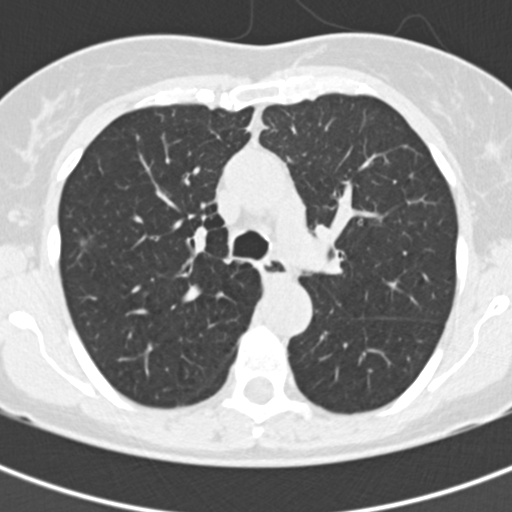
Chest CT (low-dose screening protocol), one axial image; baseline annual screen; lung window (W 1500 / L -600 HU); 2 mm slice thickness; slice 65 of 177 in the series. Female, age 60 years at enrolment. Current smoker at enrolment.
Expert-annotated lung lesion, box from (x=55, y=220) to (x=110, y=268) px. No non-calcified nodule or mass ≥4 mm was recorded by the screening reader at this exam. Official screen result: negative screen, no significant abnormalities. Lung cancer was diagnosed 861 days after this screen: bronchiolo-alveolar adenocarcinoma, NOS, right upper lobe, well differentiated (G1), stage IA (AJCC 6th edition), 11 mm at pathology.